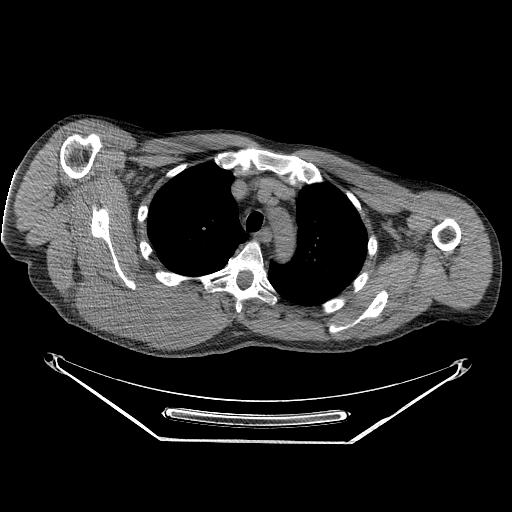
CT of an extremity soft-tissue mass (from a PET/CT study), one axial slice; position 190 of 267 along the scan axis; 140 kVp; soft-tissue window (W 400 / L 40 HU); 3.75 mm slice thickness; 512 × 512 image matrix, field of view 500 × 500 mm. Male patient. Case-level facts recorded for this patient, not image findings: histological type: pleiomorphic spindle cell undifferentiated; grade: high; site of the primary tumour: right parascapusular.
Annotated regions visible in this slice (expert contour drawn on MRI and transferred to this co-registered scan by the dataset authors):
- gross tumour volume including surrounding oedema: bounding box [x1, y1, x2, y2] px = [80, 265, 223, 339]
- gross tumour volume (mass): [80, 265, 207, 336]